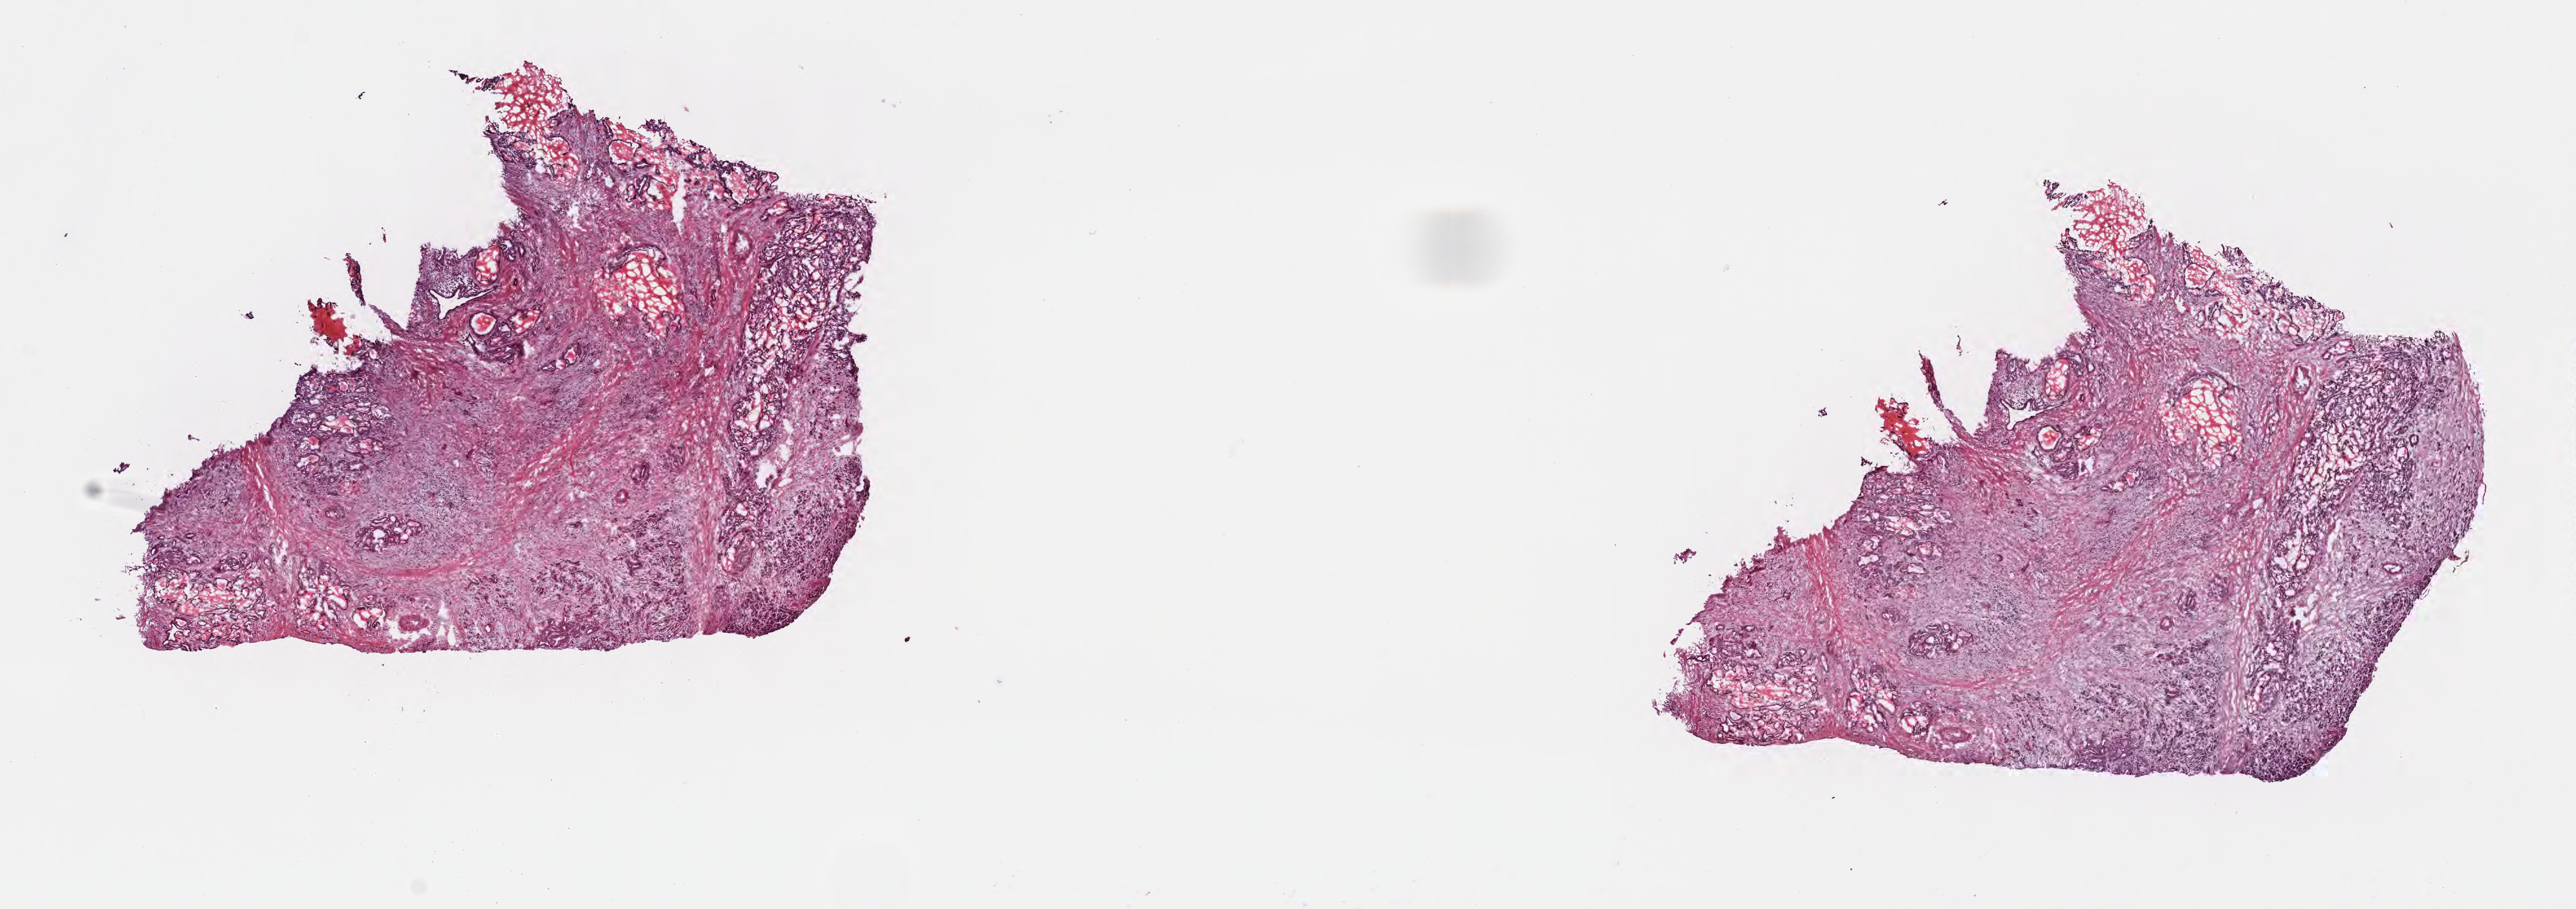
Hematoxylin and eosin (H&E) whole-slide image, whole scanned area (about 16.1 x 5.7 mm) shown as a low-resolution overview. Frozen section (tissue freezing medium). Specimen: primary tumor. Site: tail of pancreas. Female patient; age at initial diagnosis 63 years. Tumor grade: G2 (moderately differentiated). Pathologist review of this section (percent, as recorded): tumor cells 40%, tumor nuclei 40%, stromal cells 25%, necrosis 0%, normal cells 35%. Inflammatory infiltration, as recorded: lymphocyte infiltration 4%, monocyte infiltration 3%, neutrophil infiltration 8%.
Diagnosis: Infiltrating duct carcinoma, NOS. AJCC pathologic stage: Stage IIB. Section: top of the tissue portion.